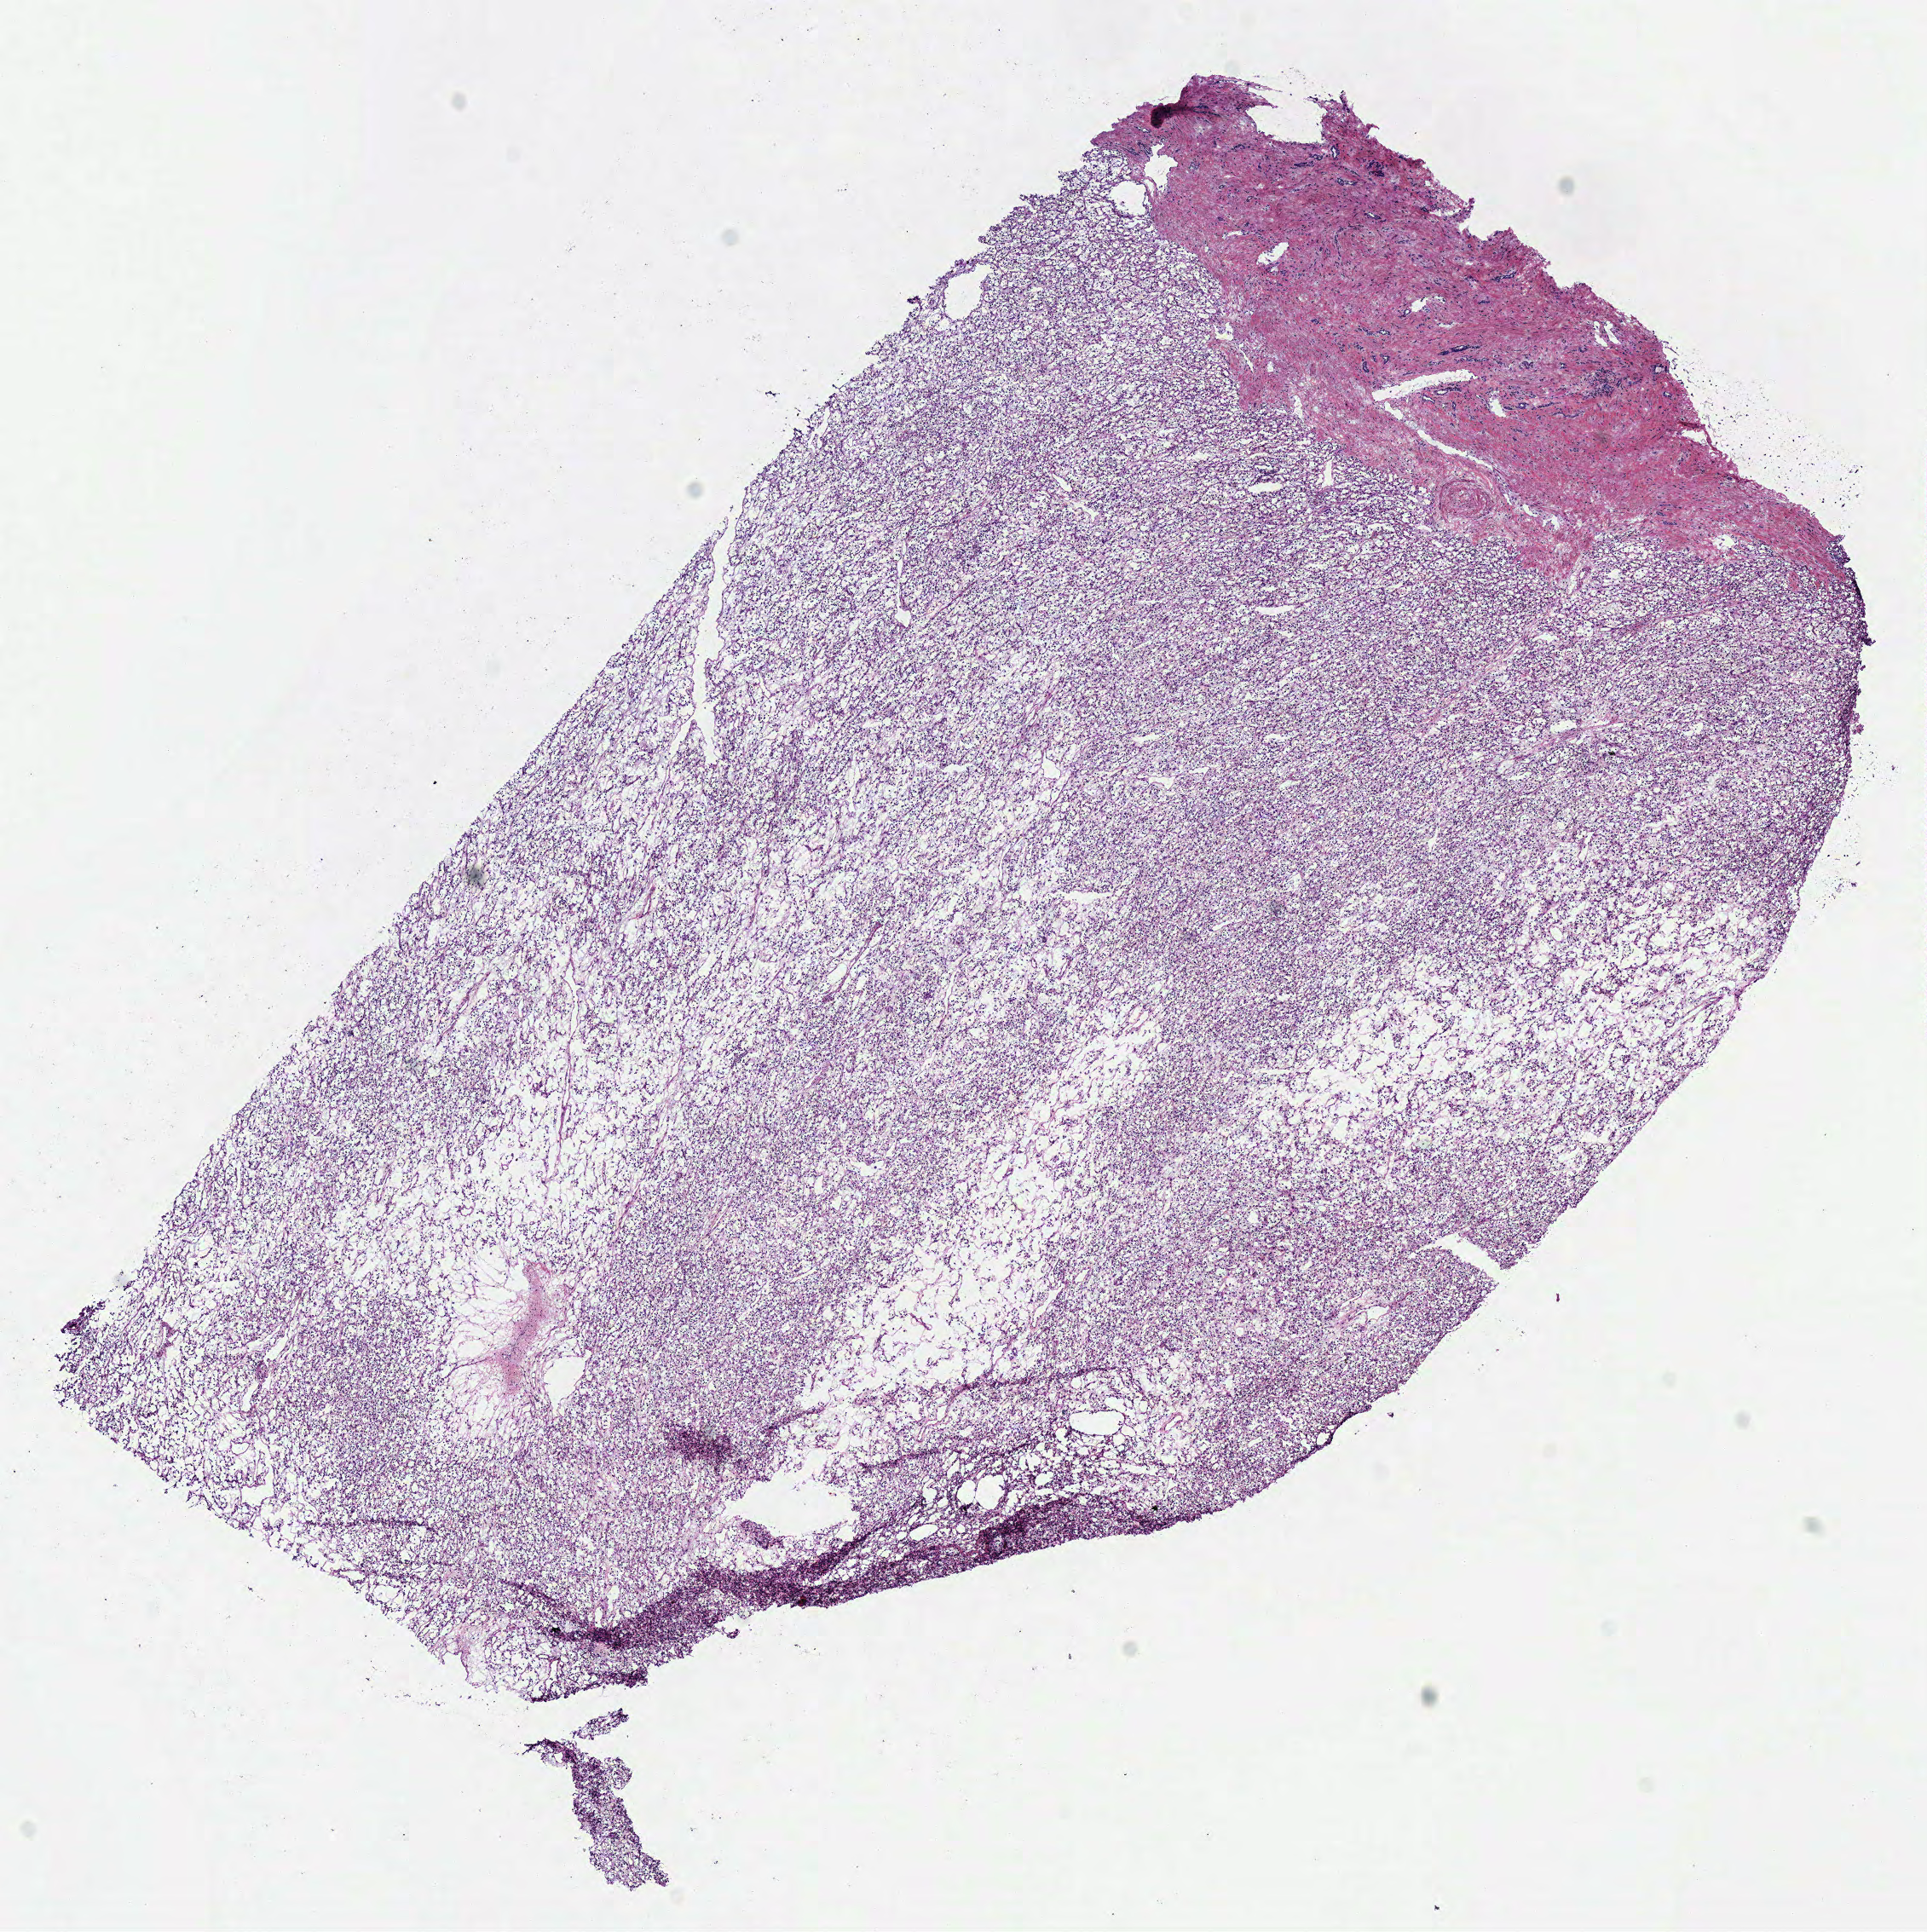
Whole-slide histology image, H&E — low-resolution overview of the scanned area, about 8.9 x 8.9 mm; frozen section from the bottom of the tissue portion; primary tumour sample from the kidney. Patient: male, age at initial diagnosis 73 years. Histologic grade: G1 (well differentiated). Pathologist review of this section (percent, as recorded): tumour cells 85%, tumour nuclei 85%, normal cells 0%, stromal cells 15%, necrosis 0%.
Pathologic diagnosis: Clear cell adenocarcinoma, NOS. AJCC pathologic stage: I.